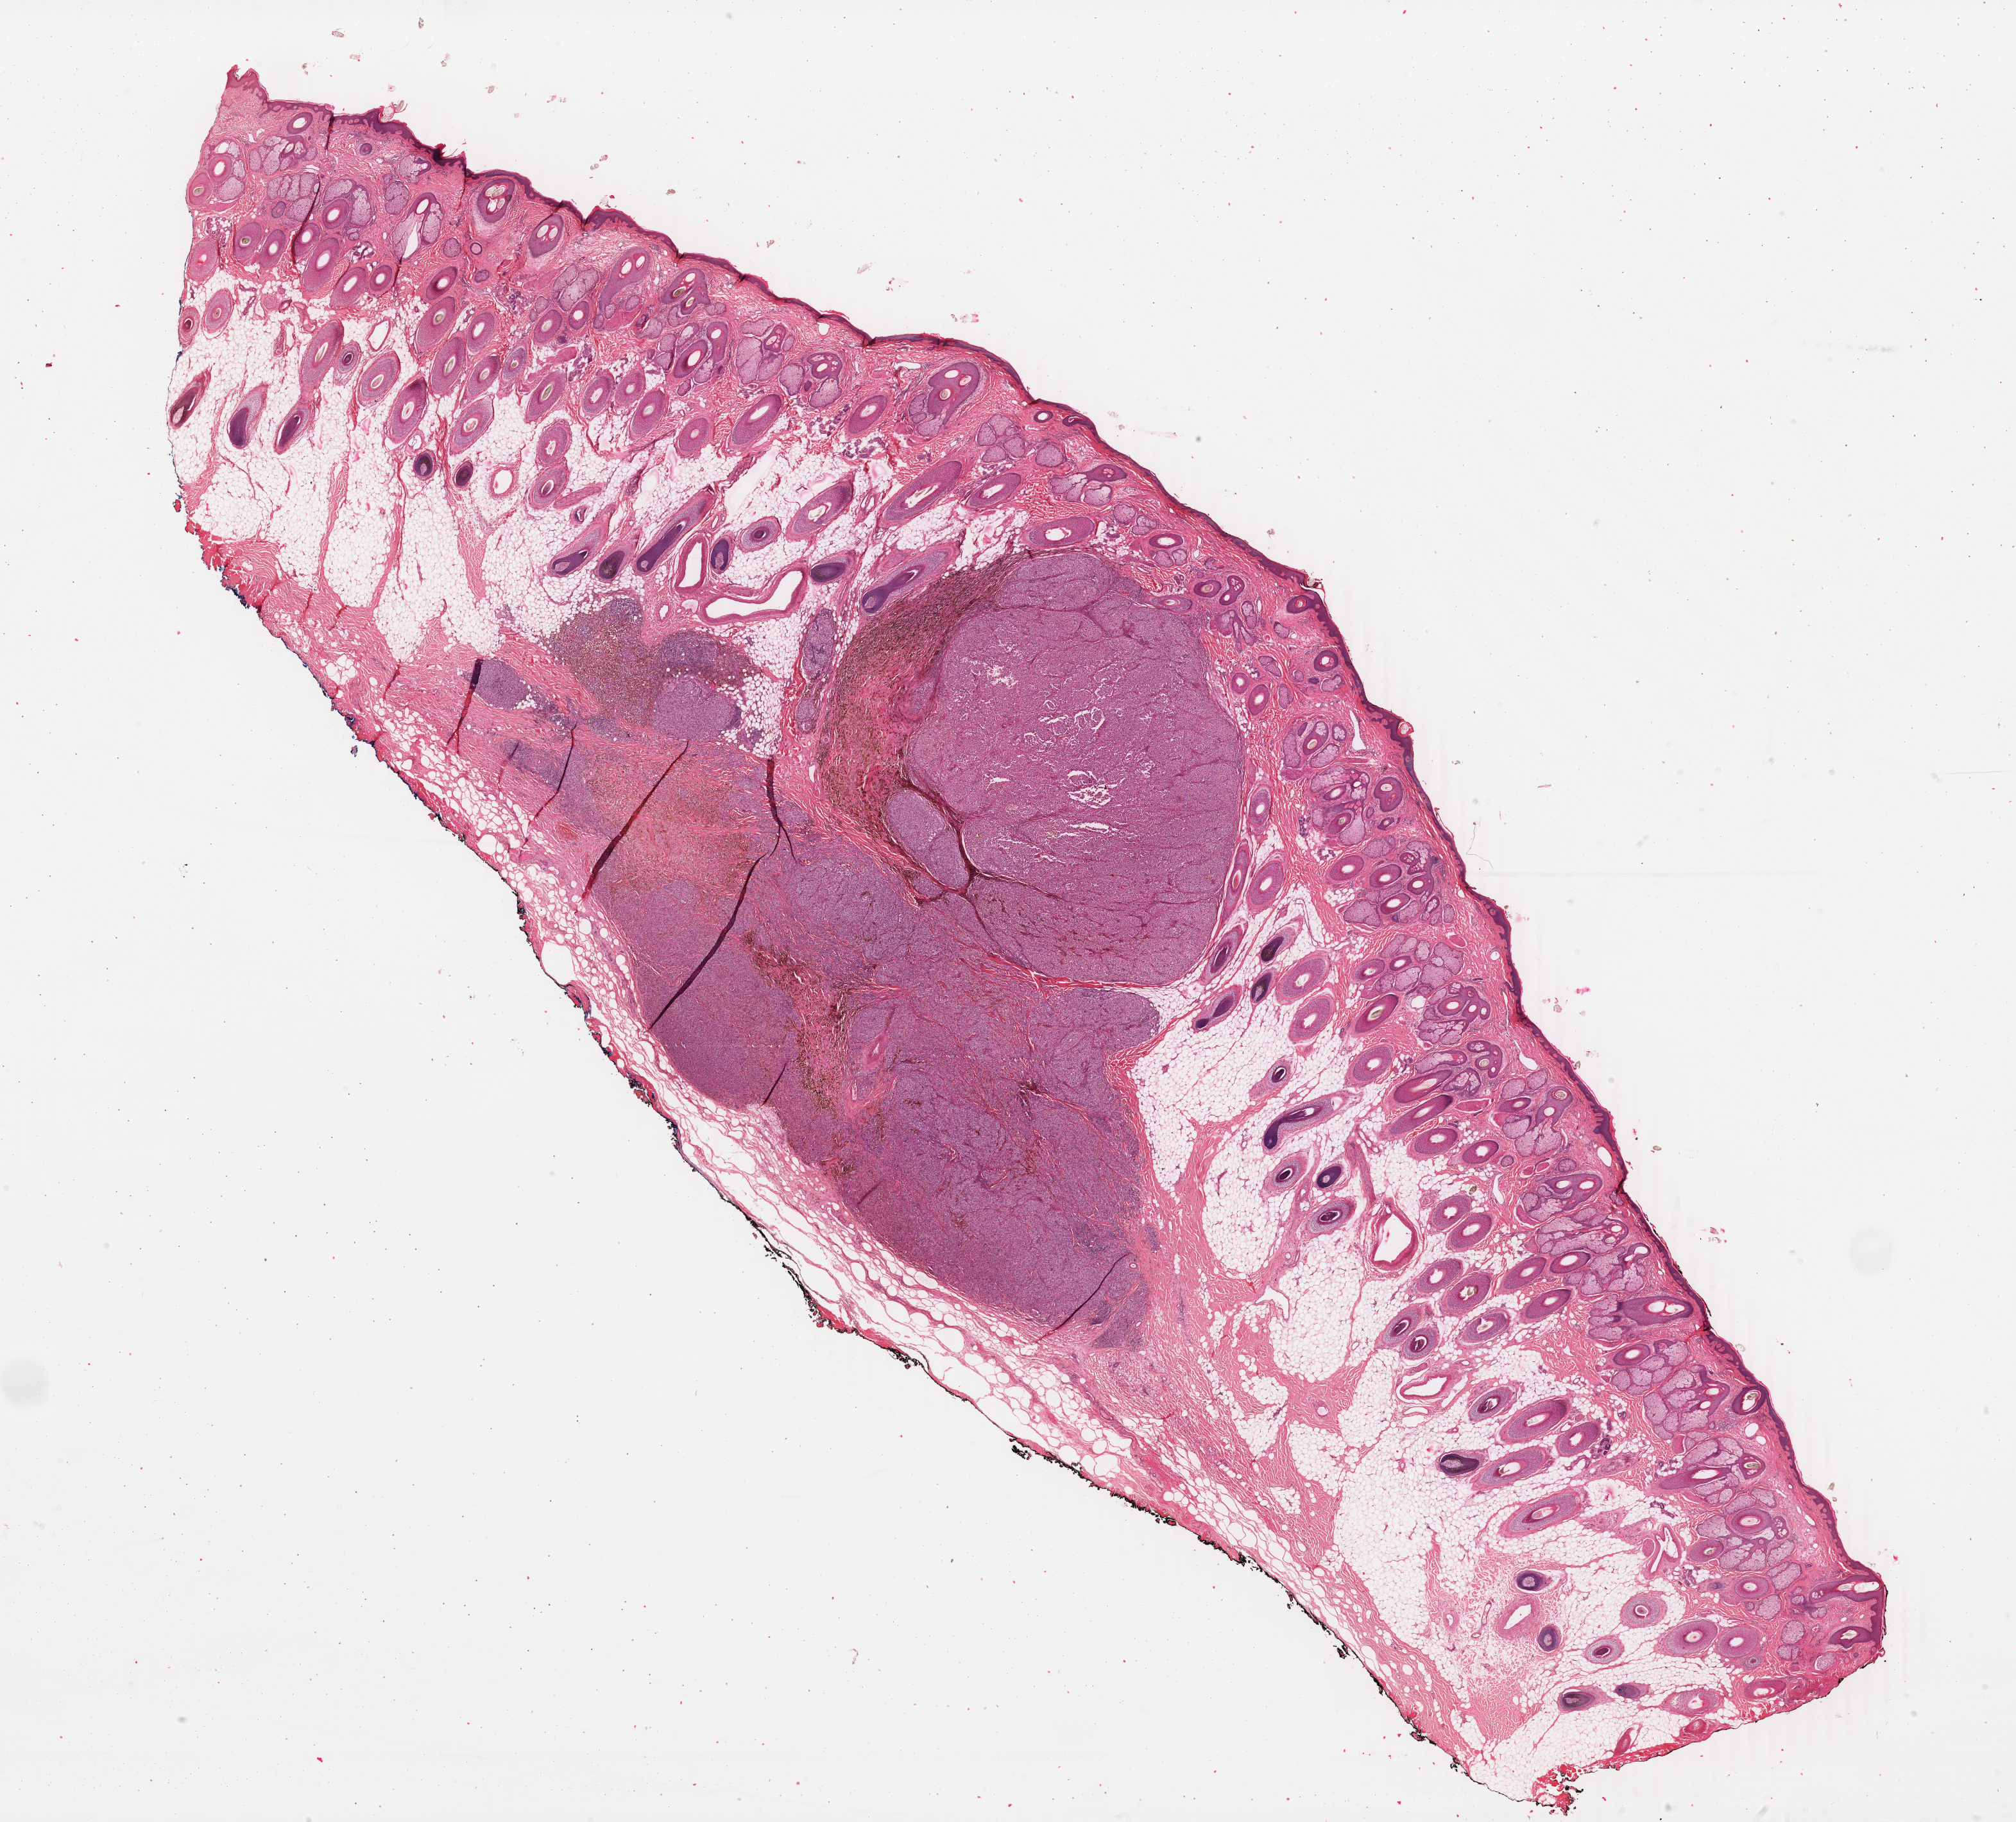
Whole-slide histology image, H&E, whole scanned area (about 25.0 x 22.6 mm) shown as a low-resolution overview, formalin-fixed paraffin-embedded (FFPE) diagnostic section, skin, primary tumour sample. Male patient; age at initial diagnosis 53 years.
Pathologic diagnosis: Malignant melanoma, NOS.